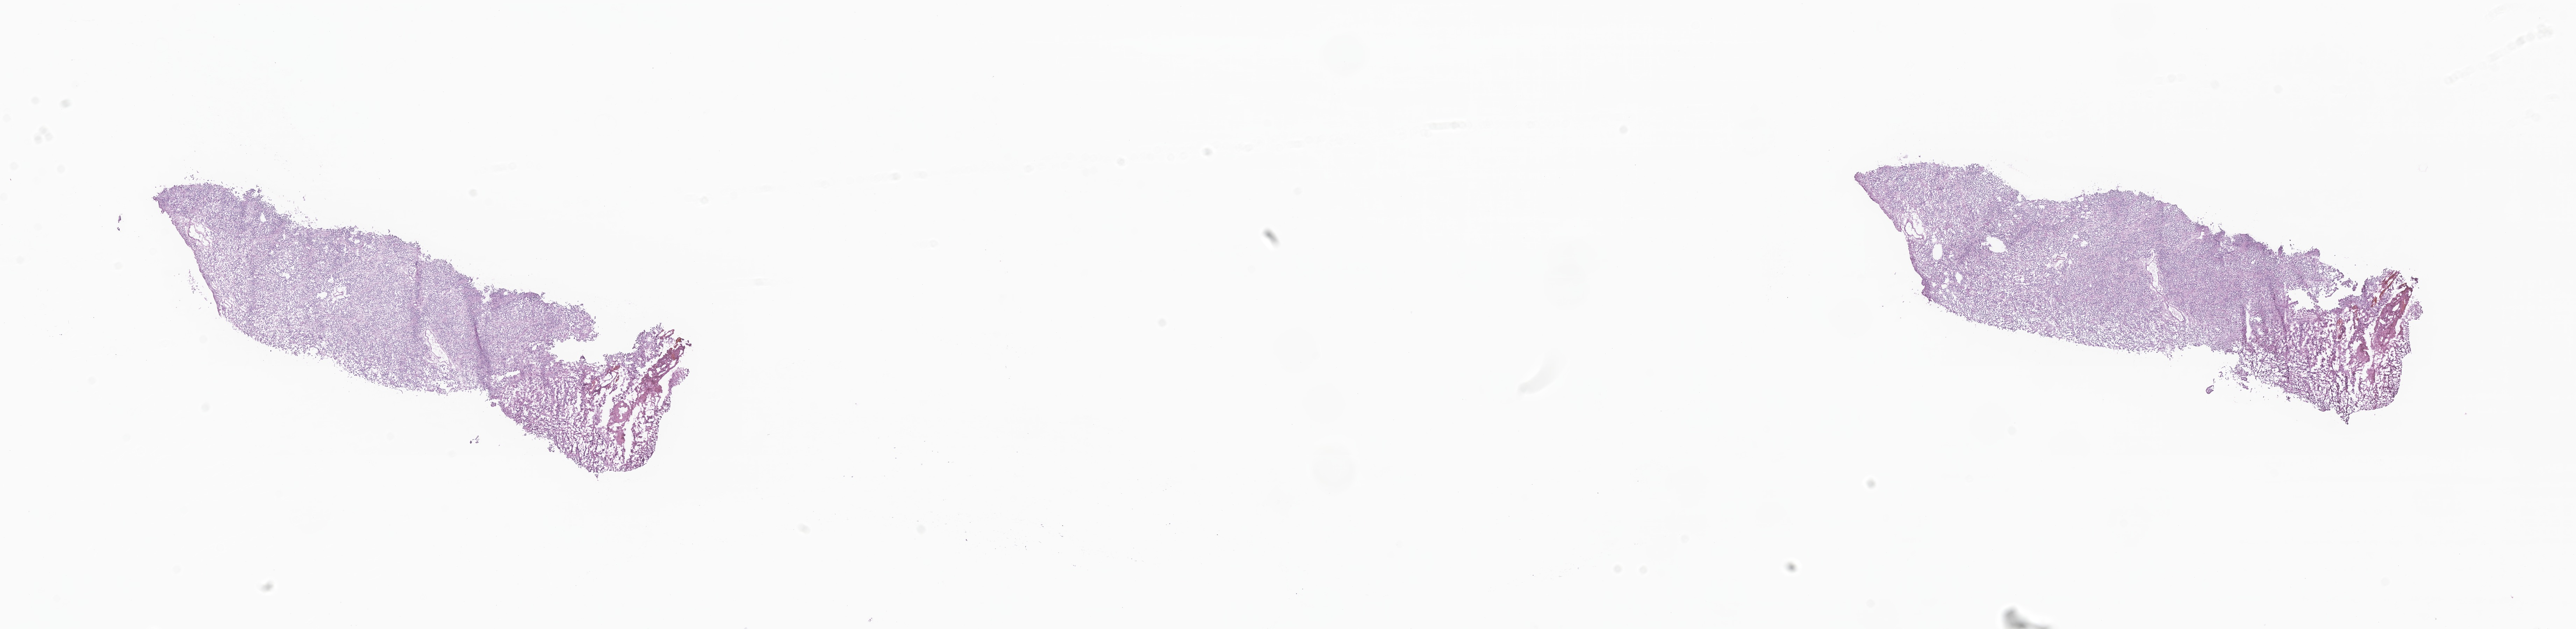
Whole-slide image, hematoxylin and eosin (H&E) stain of tumor tissue from the frontal lobe, a low-resolution overview of the entire scanned area, about 31.1 x 7.6 mm; cryosection (OCT / tissue freezing medium). Patient male; age 83 months (6 years 11 months).
• diagnosis (ICD-O-3 morphology term): Ependymoma, NOS